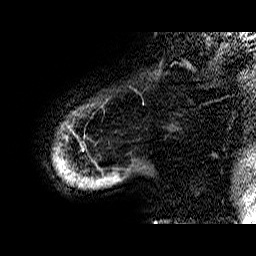
Breast MRI (dynamic contrast-enhanced), one sagittal slice; position 3 of 60 along the scan axis; dynamic contrast-enhanced series, time point 2 of 6 at this slice position (early post-contrast); 1.5 T; TE 6.4 ms, TR 32.9 ms; 4 mm slice thickness; 256 × 256 image matrix, field of view 200 × 200 mm. Female patient. Case-level facts recorded for this patient, not image findings: setting: breast cancer imaged before/during neoadjuvant chemotherapy; receptor status: HR-positive, HER2-negative.
Structures marked on this image (semi-automatic segmentation, software-assisted and operator-edited):
- analysis volume of interest (the breast-tissue region the enhancement analysis was run in; not a lesion): box from (x=53, y=75) to (x=153, y=189) px
- tumour enhancement mask (voxels above the 100 % enhancement threshold inside the analysis volume of interest): (x=55, y=149)–(x=84, y=177)